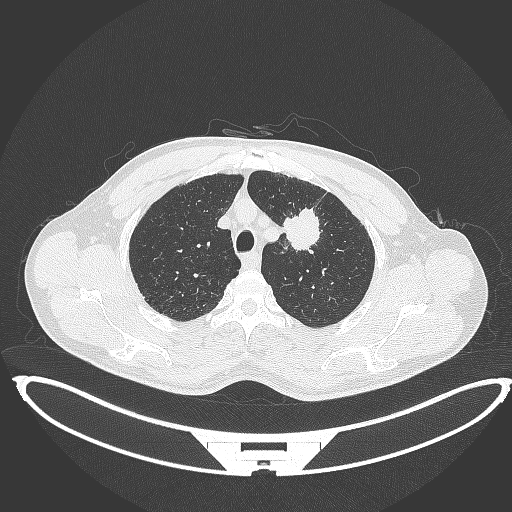
Chest CT, one axial slice. Position 354 of 395 along the scan axis. Reconstruction kernel B70f. 120 kVp. Lung window (W 1500 / L -600 HU). 512 × 512 image matrix. Male patient, age 60 years. From the clinical record (not read from this slice): clinical TNM (as recorded): T2a N0 M0.
Structures marked on this image (bounding box drawn by a radiologist):
- lung tumour (recorded histology: squamous cell carcinoma): box from (x=281, y=201) to (x=325, y=253) px